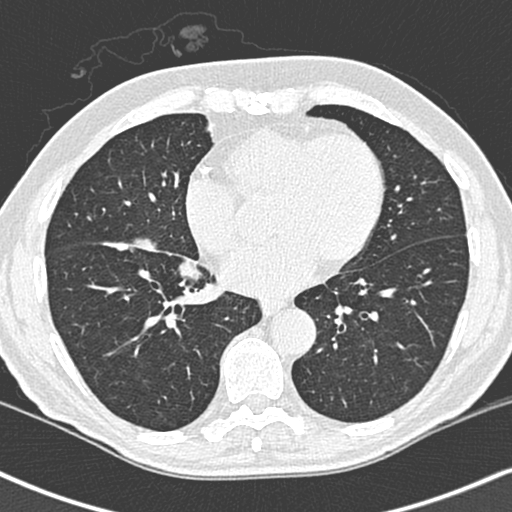
Low-dose screening chest CT, one axial slice. Slice 110 of 248 in the series (ordered by position). 120 kVp. Lung window (W 1500 / L -600 HU). 1.3 mm slice thickness. 512 × 512 image matrix, field of view 323 × 323 mm.
Outlined on this slice (manually delineated by an expert):
- lesion 1 (tumor, lower lobe of right lung): box from (x=102, y=201) to (x=156, y=214) px